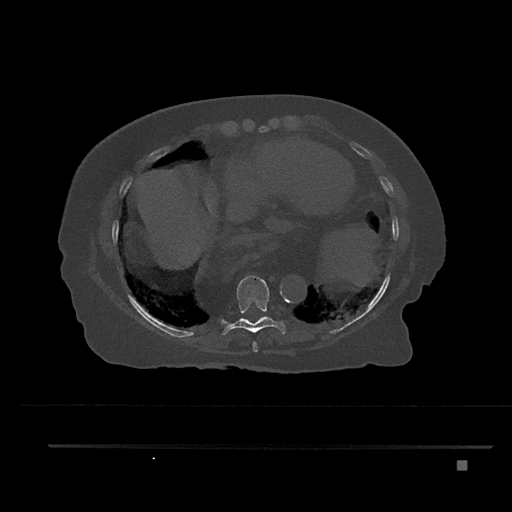
CT including the spine, one axial slice. Reconstruction kernel Br40s/3. 120 kVp. Bone window (W 1800 / L 400 HU). 512 × 512 image matrix, field of view 437 × 437 mm. Patient: female, 76 years. Case-level facts recorded for this patient, not image findings: primary cancer: lung; vertebrae with lytic lesions (as recorded): T11, L3.
Outlined on this slice (semi-automatically segmented with operator editing):
- T8 vertebra: bounding box <253,340,258,352> (left, top, right, bottom; pixels)
- T9 vertebra: <221,276,287,335>